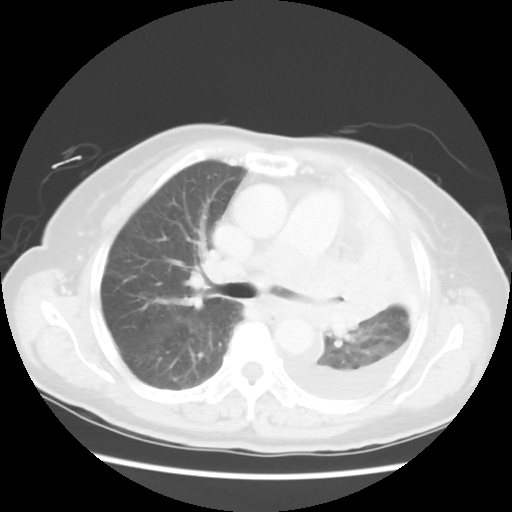
Chest CT, one axial slice; slice 34 of 52 in the series (ordered by position); reconstruction kernel STANDARD; lung window (W 1500 / L -600 HU); 512 × 512 image matrix, field of view 336 × 336 mm. Female patient, age 72 years. From the clinical record (not read from this slice): clinical TNM (as recorded): T4 N3 M1b.
Annotated regions visible in this slice (bounding box drawn by a radiologist):
- lung tumour (recorded histology: large cell carcinoma): box from (x=306, y=245) to (x=398, y=346) px